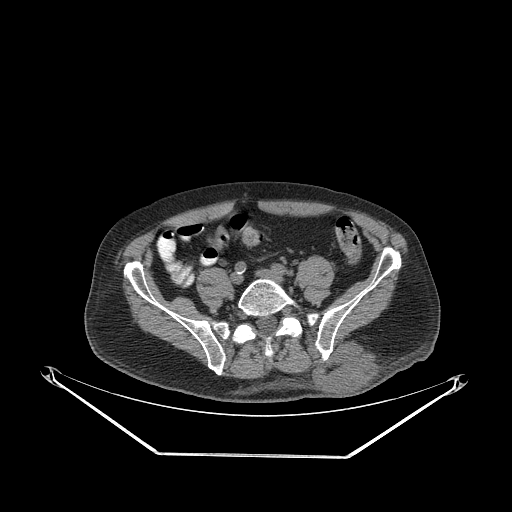
CT of an extremity soft-tissue mass (from a PET/CT study), one axial slice. Position 84 of 267 along the scan axis. Reconstruction kernel STANDARD. 140 kVp. Soft-tissue window (W 400 / L 40 HU). 3.75 mm slice thickness. 512 × 512 image matrix, field of view 500 × 500 mm. Male patient. Case-level facts recorded for this patient, not image findings: histological type: leiomyosarcoma; grade: intermediate; site of the primary tumour: left pelvis.
Outlined on this slice (expert contour drawn on MRI and transferred to this co-registered scan by the dataset authors):
- gross tumour volume (mass): bounding box (x1, y1, x2, y2) in pixels: (313, 340, 380, 394)